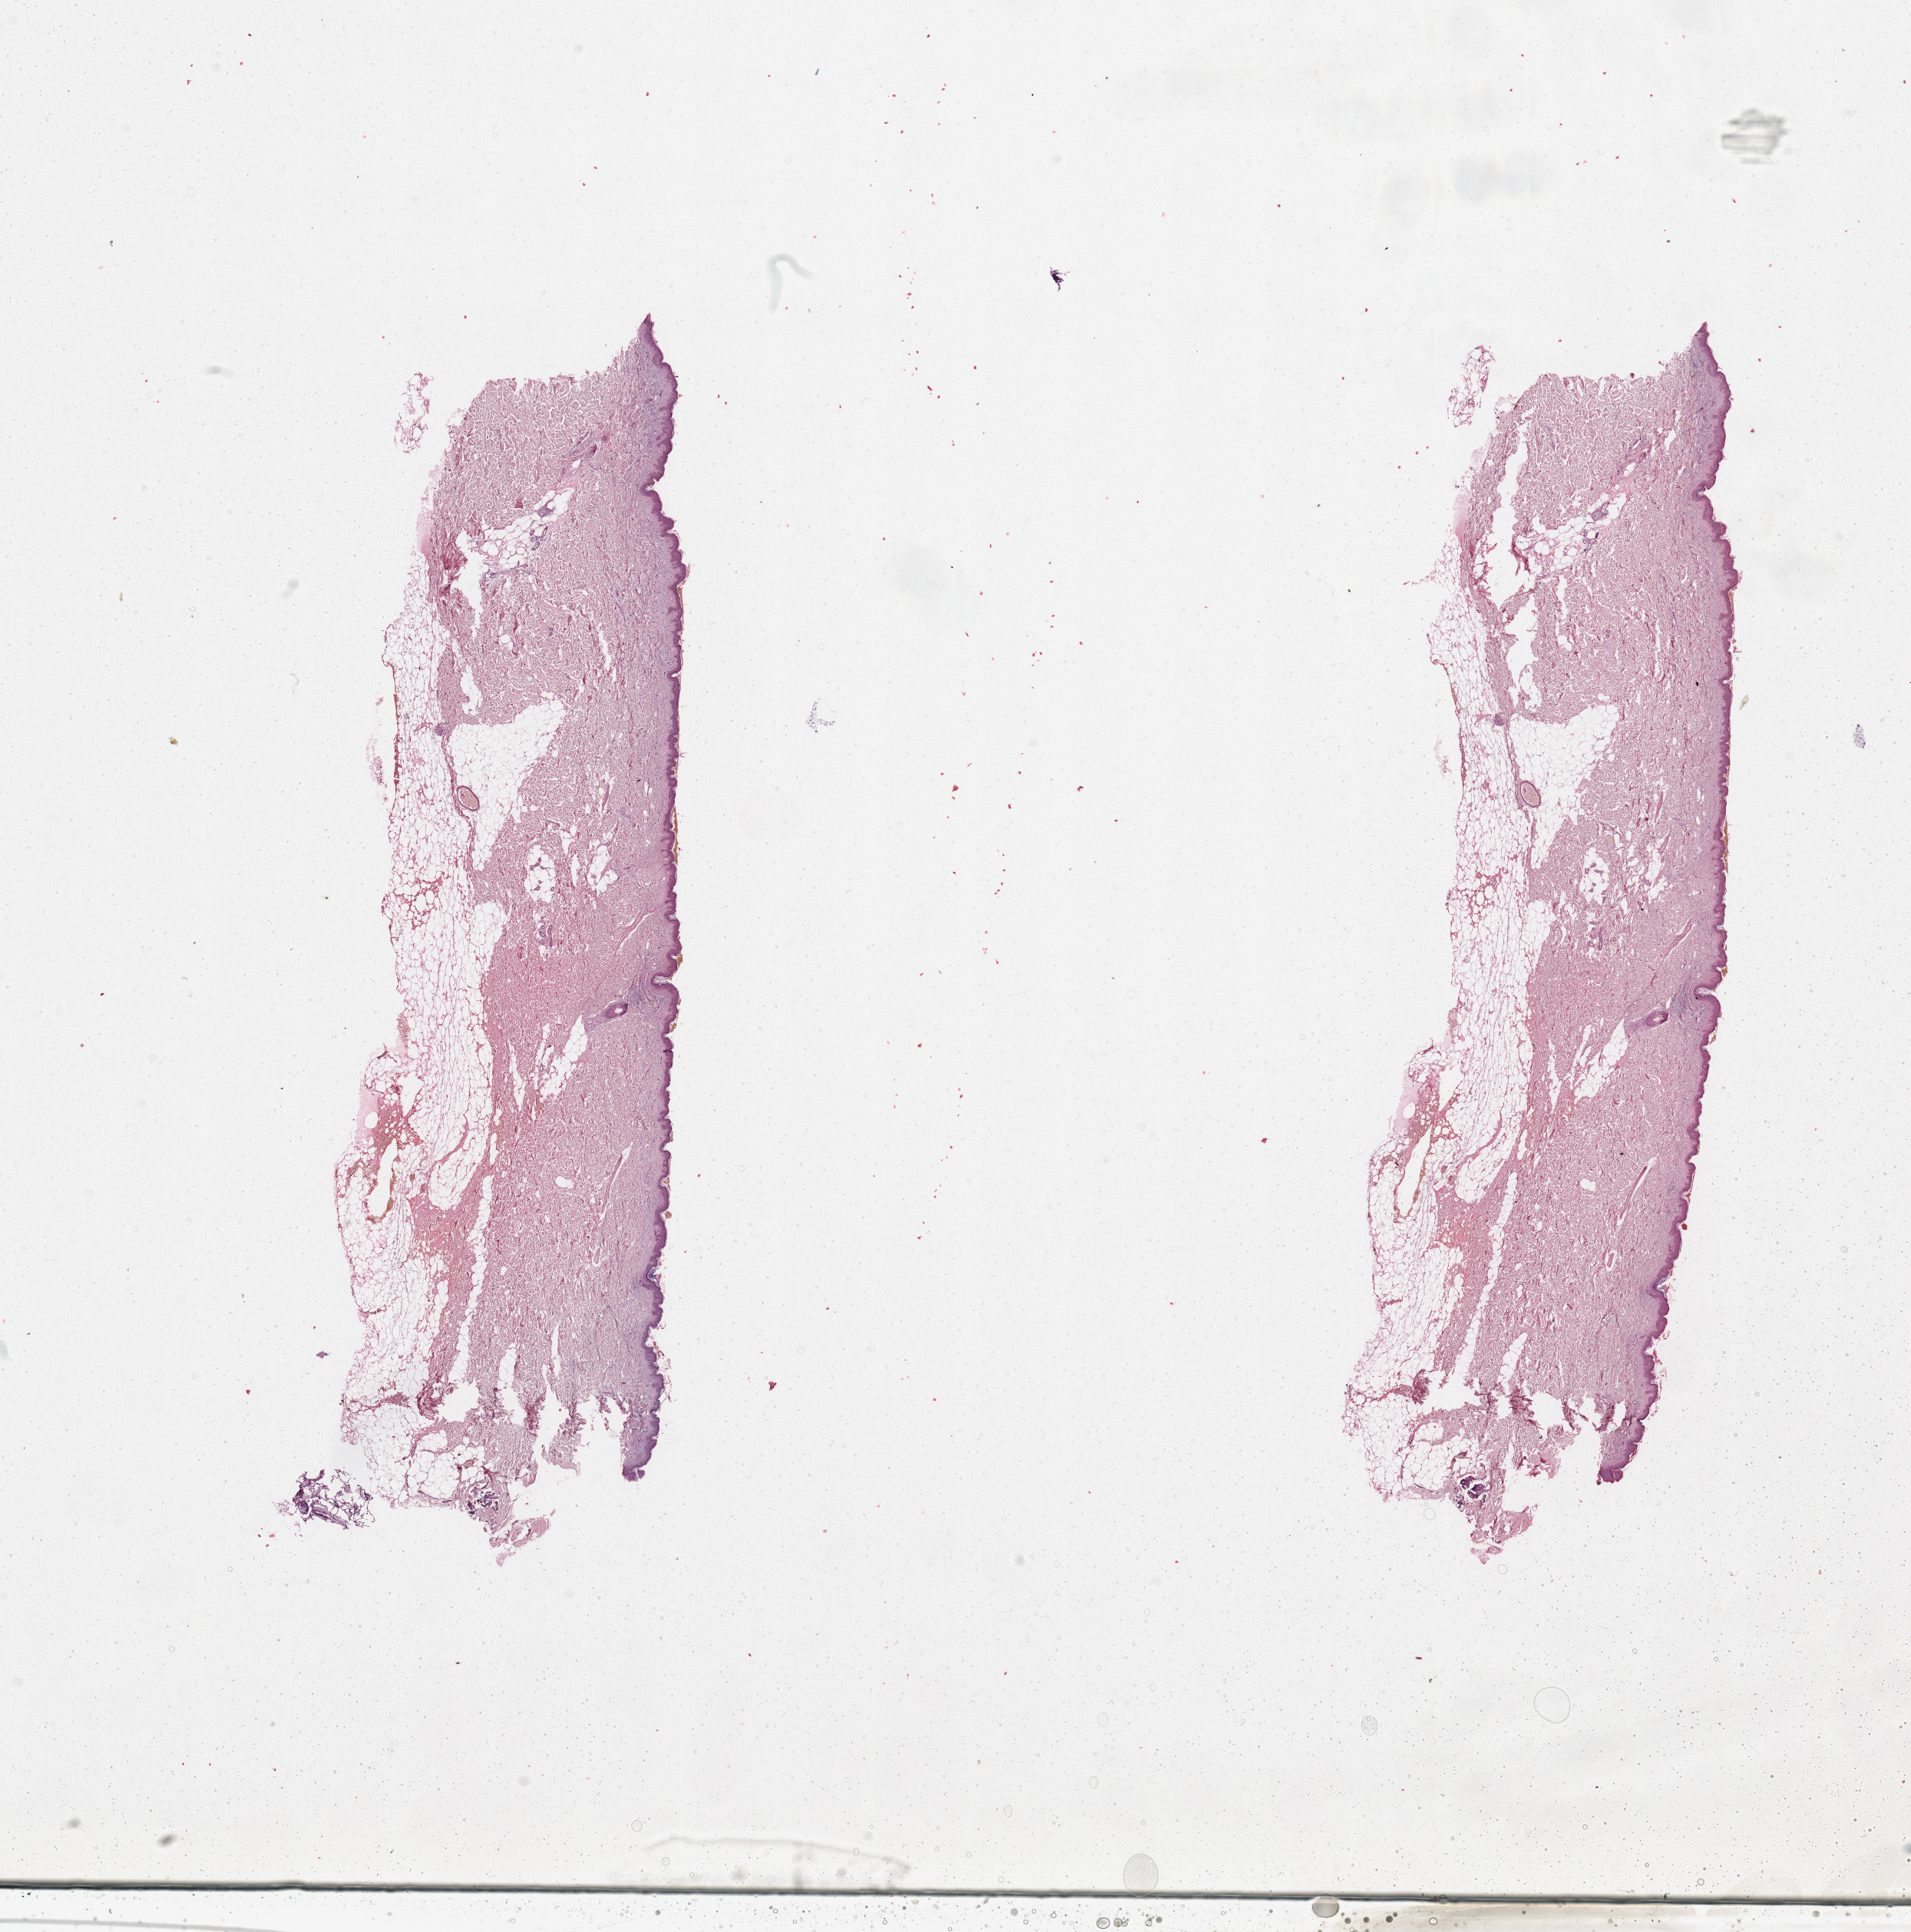
Digitized H&E-stained tissue section (whole slide), a low-resolution overview of the entire scanned area, about 19.7 x 19.9 mm, normal (non-tumour) tissue sample, sampled site: shoulder. 45-year-old female patient.
- this section: normal (non-tumour) tissue from the same patient
- patient diagnosis: Malignant melanoma, NOS